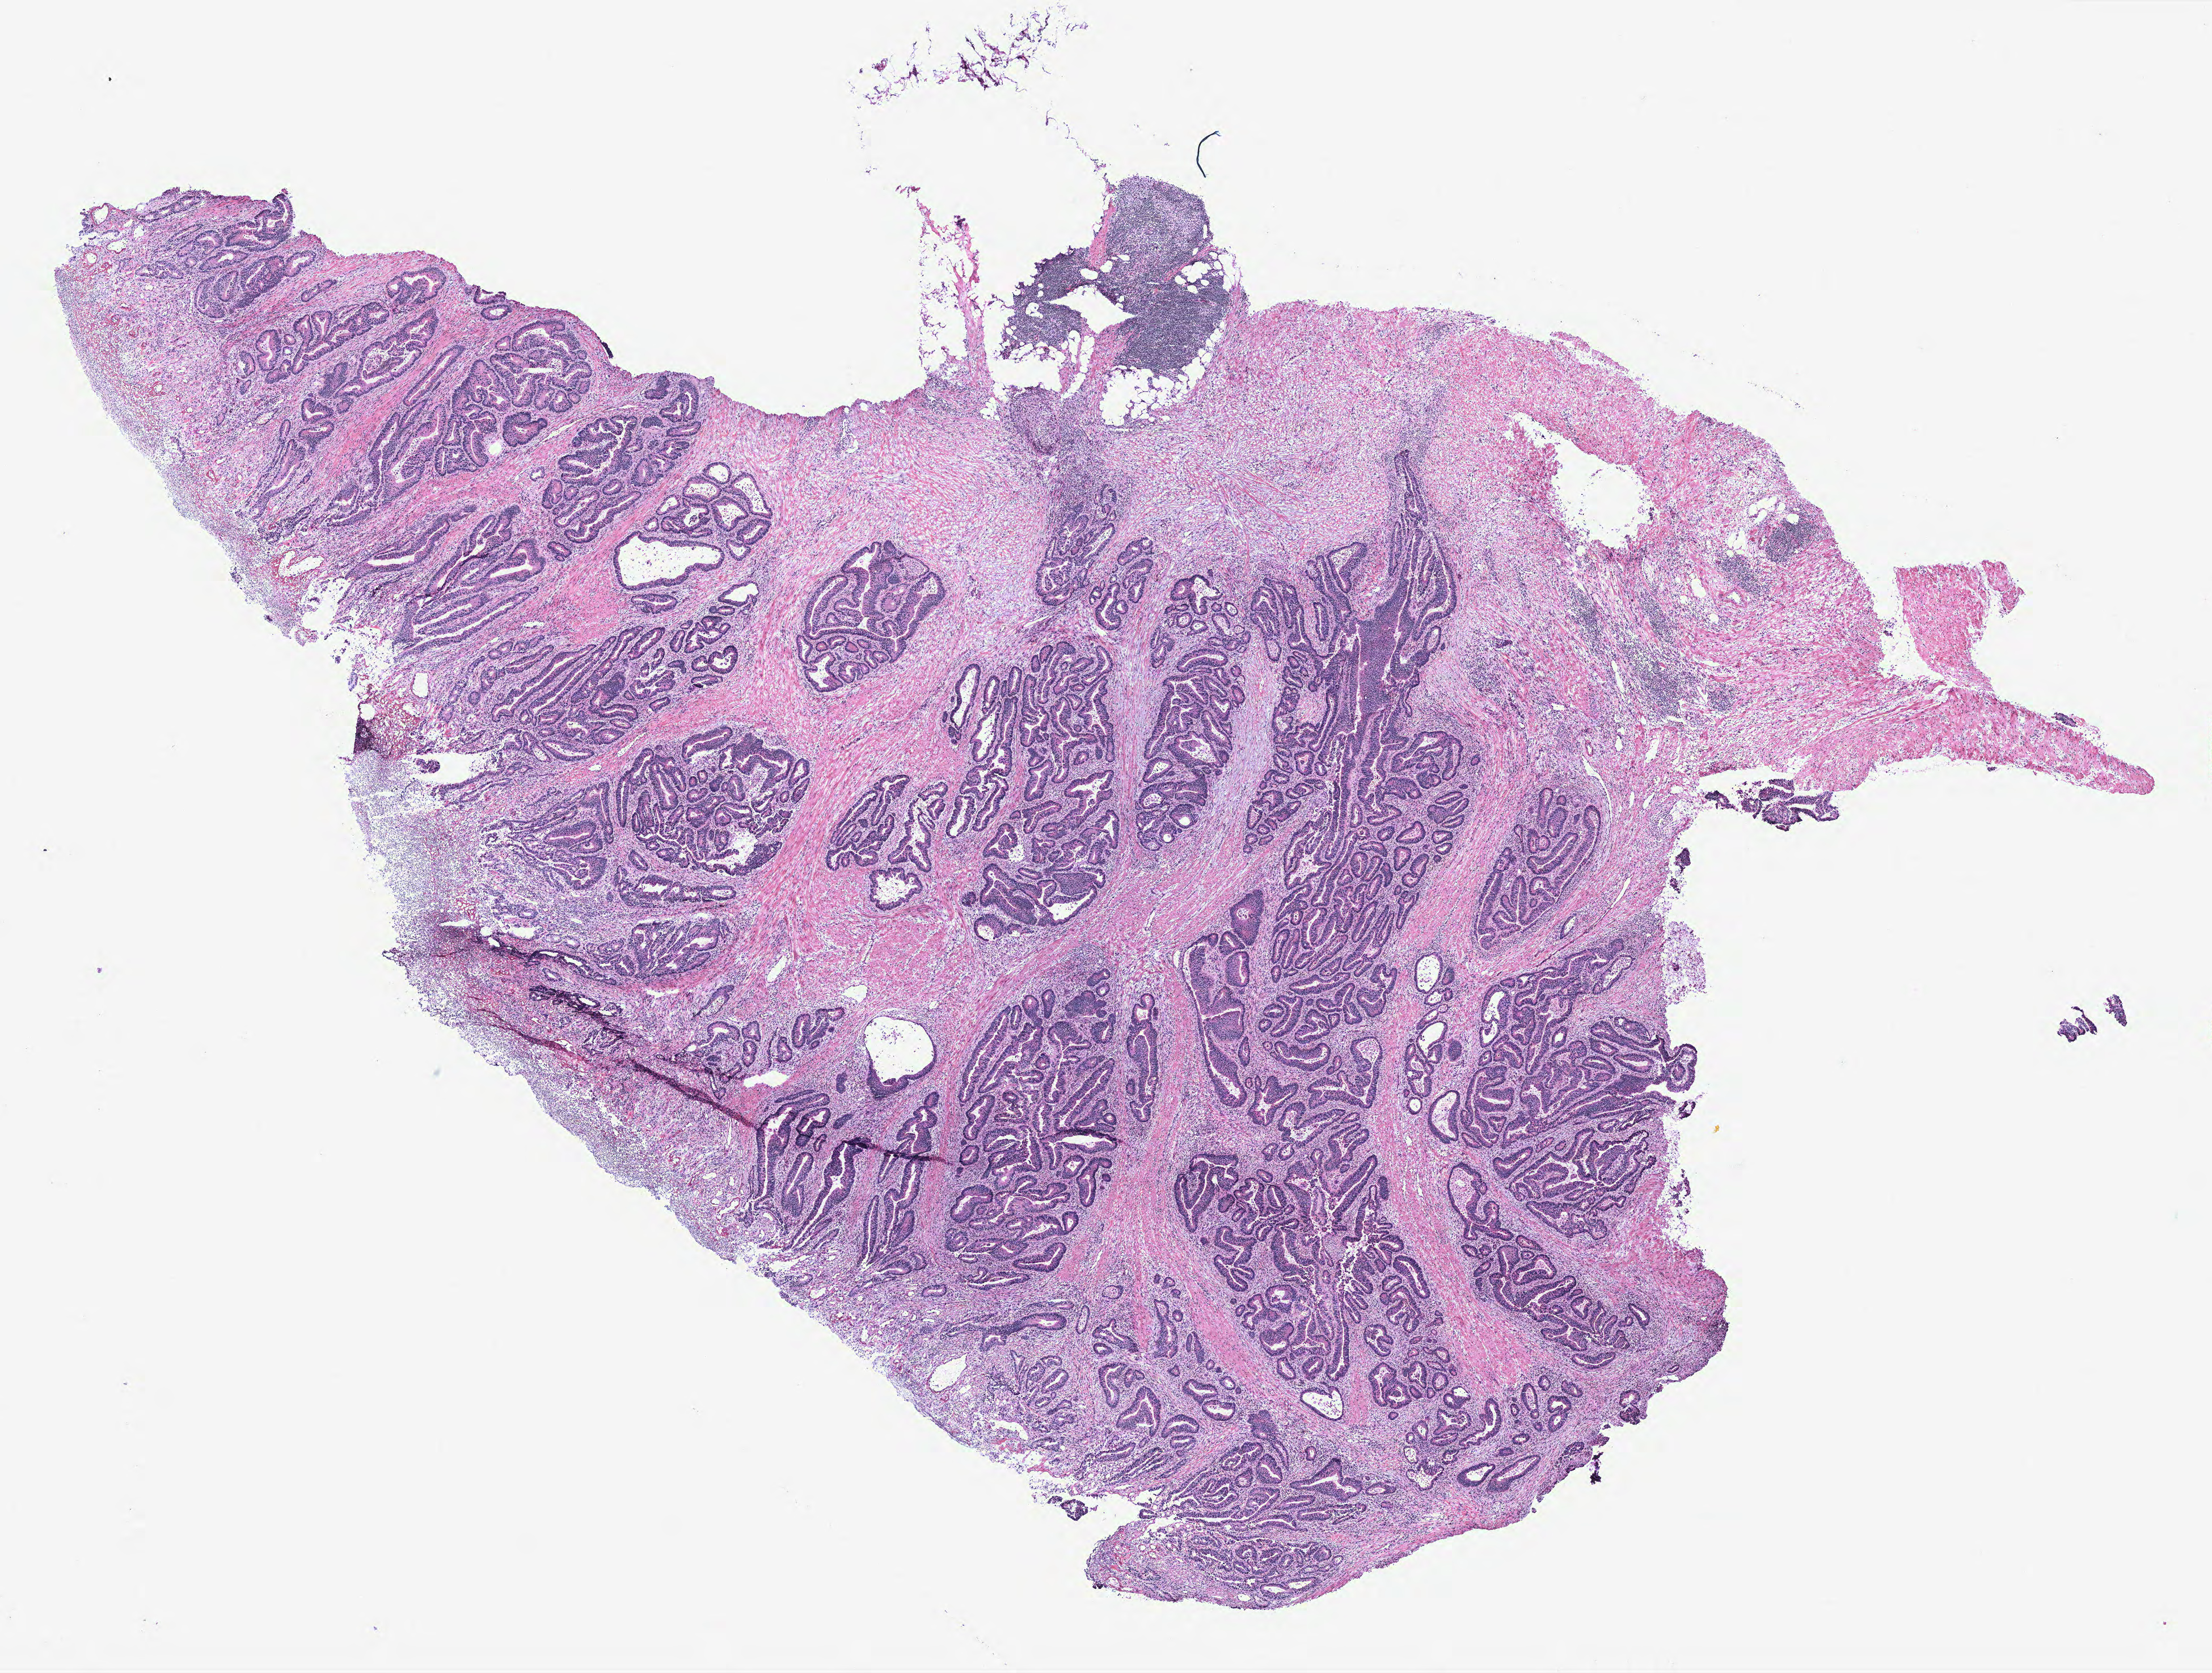
H&E-stained whole-slide image, a low-resolution overview of the entire scanned area, about 15.6 x 11.8 mm; colon, normal (non-tumour) tissue. Patient: male, age 66 years.
This section: normal (non-tumour) tissue from the same patient. Patient diagnosis: Adenocarcinoma, NOS.